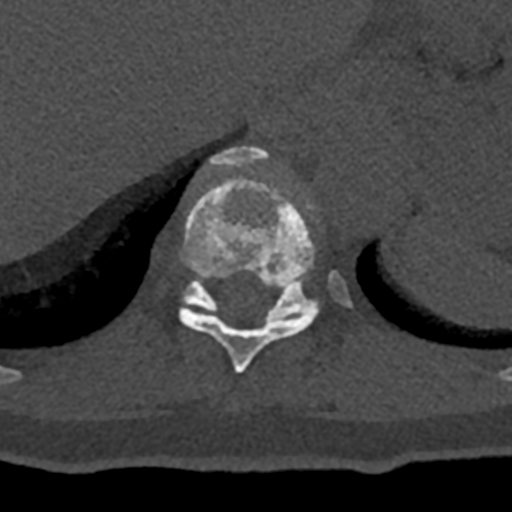
CT including the spine, one axial slice; slice 586 of 797 in the series (ordered by position); bone window (W 1800 / L 400 HU); 0.5 mm slice thickness; 512 × 512 image matrix, field of view 160 × 160 mm. Patient: male, 74 years. Case-level facts recorded for this patient, not image findings: primary cancer: renal; vertebrae with lytic lesions (as recorded): T10, L1, L2, L3, L4, L5.
Structures marked on this image (semi-automatic segmentation, software-assisted and operator-edited):
- T10 vertebra: bounding box <179,146,318,374> (left, top, right, bottom; pixels)
- T11 vertebra: <182,270,352,319>